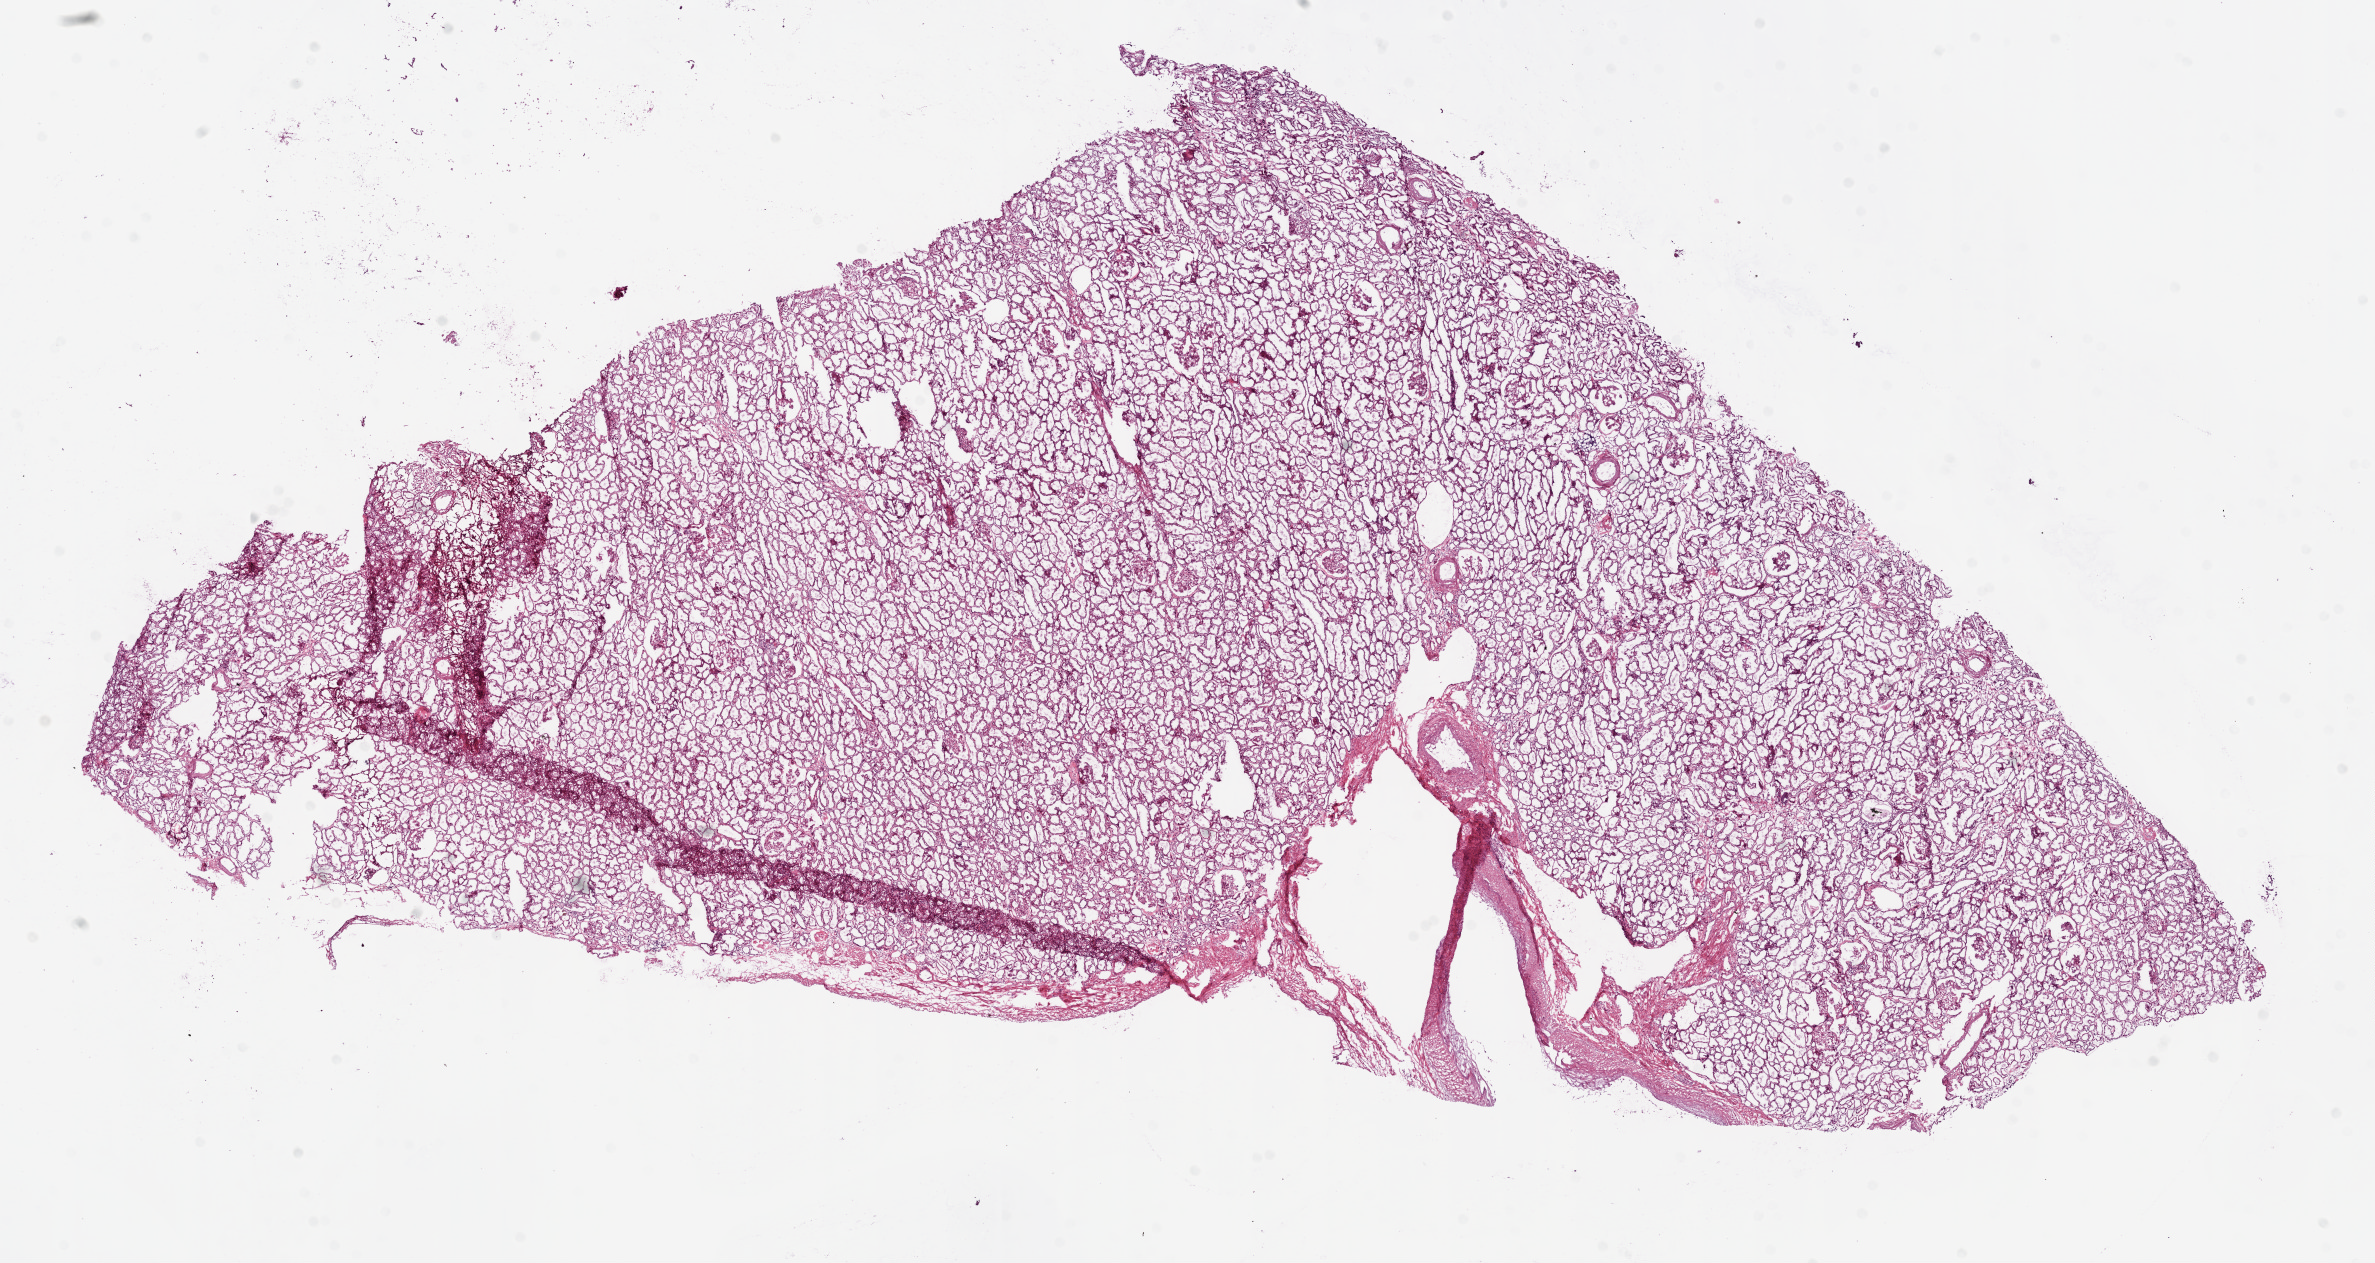
Digitized H&E tissue section (whole slide), low-resolution overview of the scanned area, about 19.1 x 10.1 mm (acquisition: 20x scan), frozen section from the bottom of the tissue portion, sample: solid tissue normal (non-tumour tissue), kidney. Patient: female, age at initial diagnosis 49 years.
* this section: solid tissue normal sample (biorepository sample class)
* patient diagnosis: Clear cell adenocarcinoma, NOS